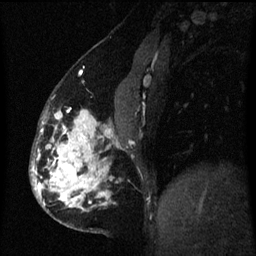
Breast MRI (dynamic contrast-enhanced), one sagittal slice. Slice 23 of 60 in the series (ordered by position). Dynamic contrast-enhanced series, image 2 of 3 at this slice position (ordered by acquisition). 1.5 T. TE 4.2 ms, TR 8 ms. 256 × 256 image matrix. Female patient, age 50 years.
Structures marked on this image (semi-automatic segmentation, software-assisted and operator-edited):
- analysis volume of interest (the breast-tissue region the enhancement analysis was run in; not a lesion): box from (x=32, y=108) to (x=120, y=230) px
- tumour enhancement mask (voxels above the 70 % enhancement threshold inside the analysis volume of interest): (x=32, y=110)–(x=111, y=207)